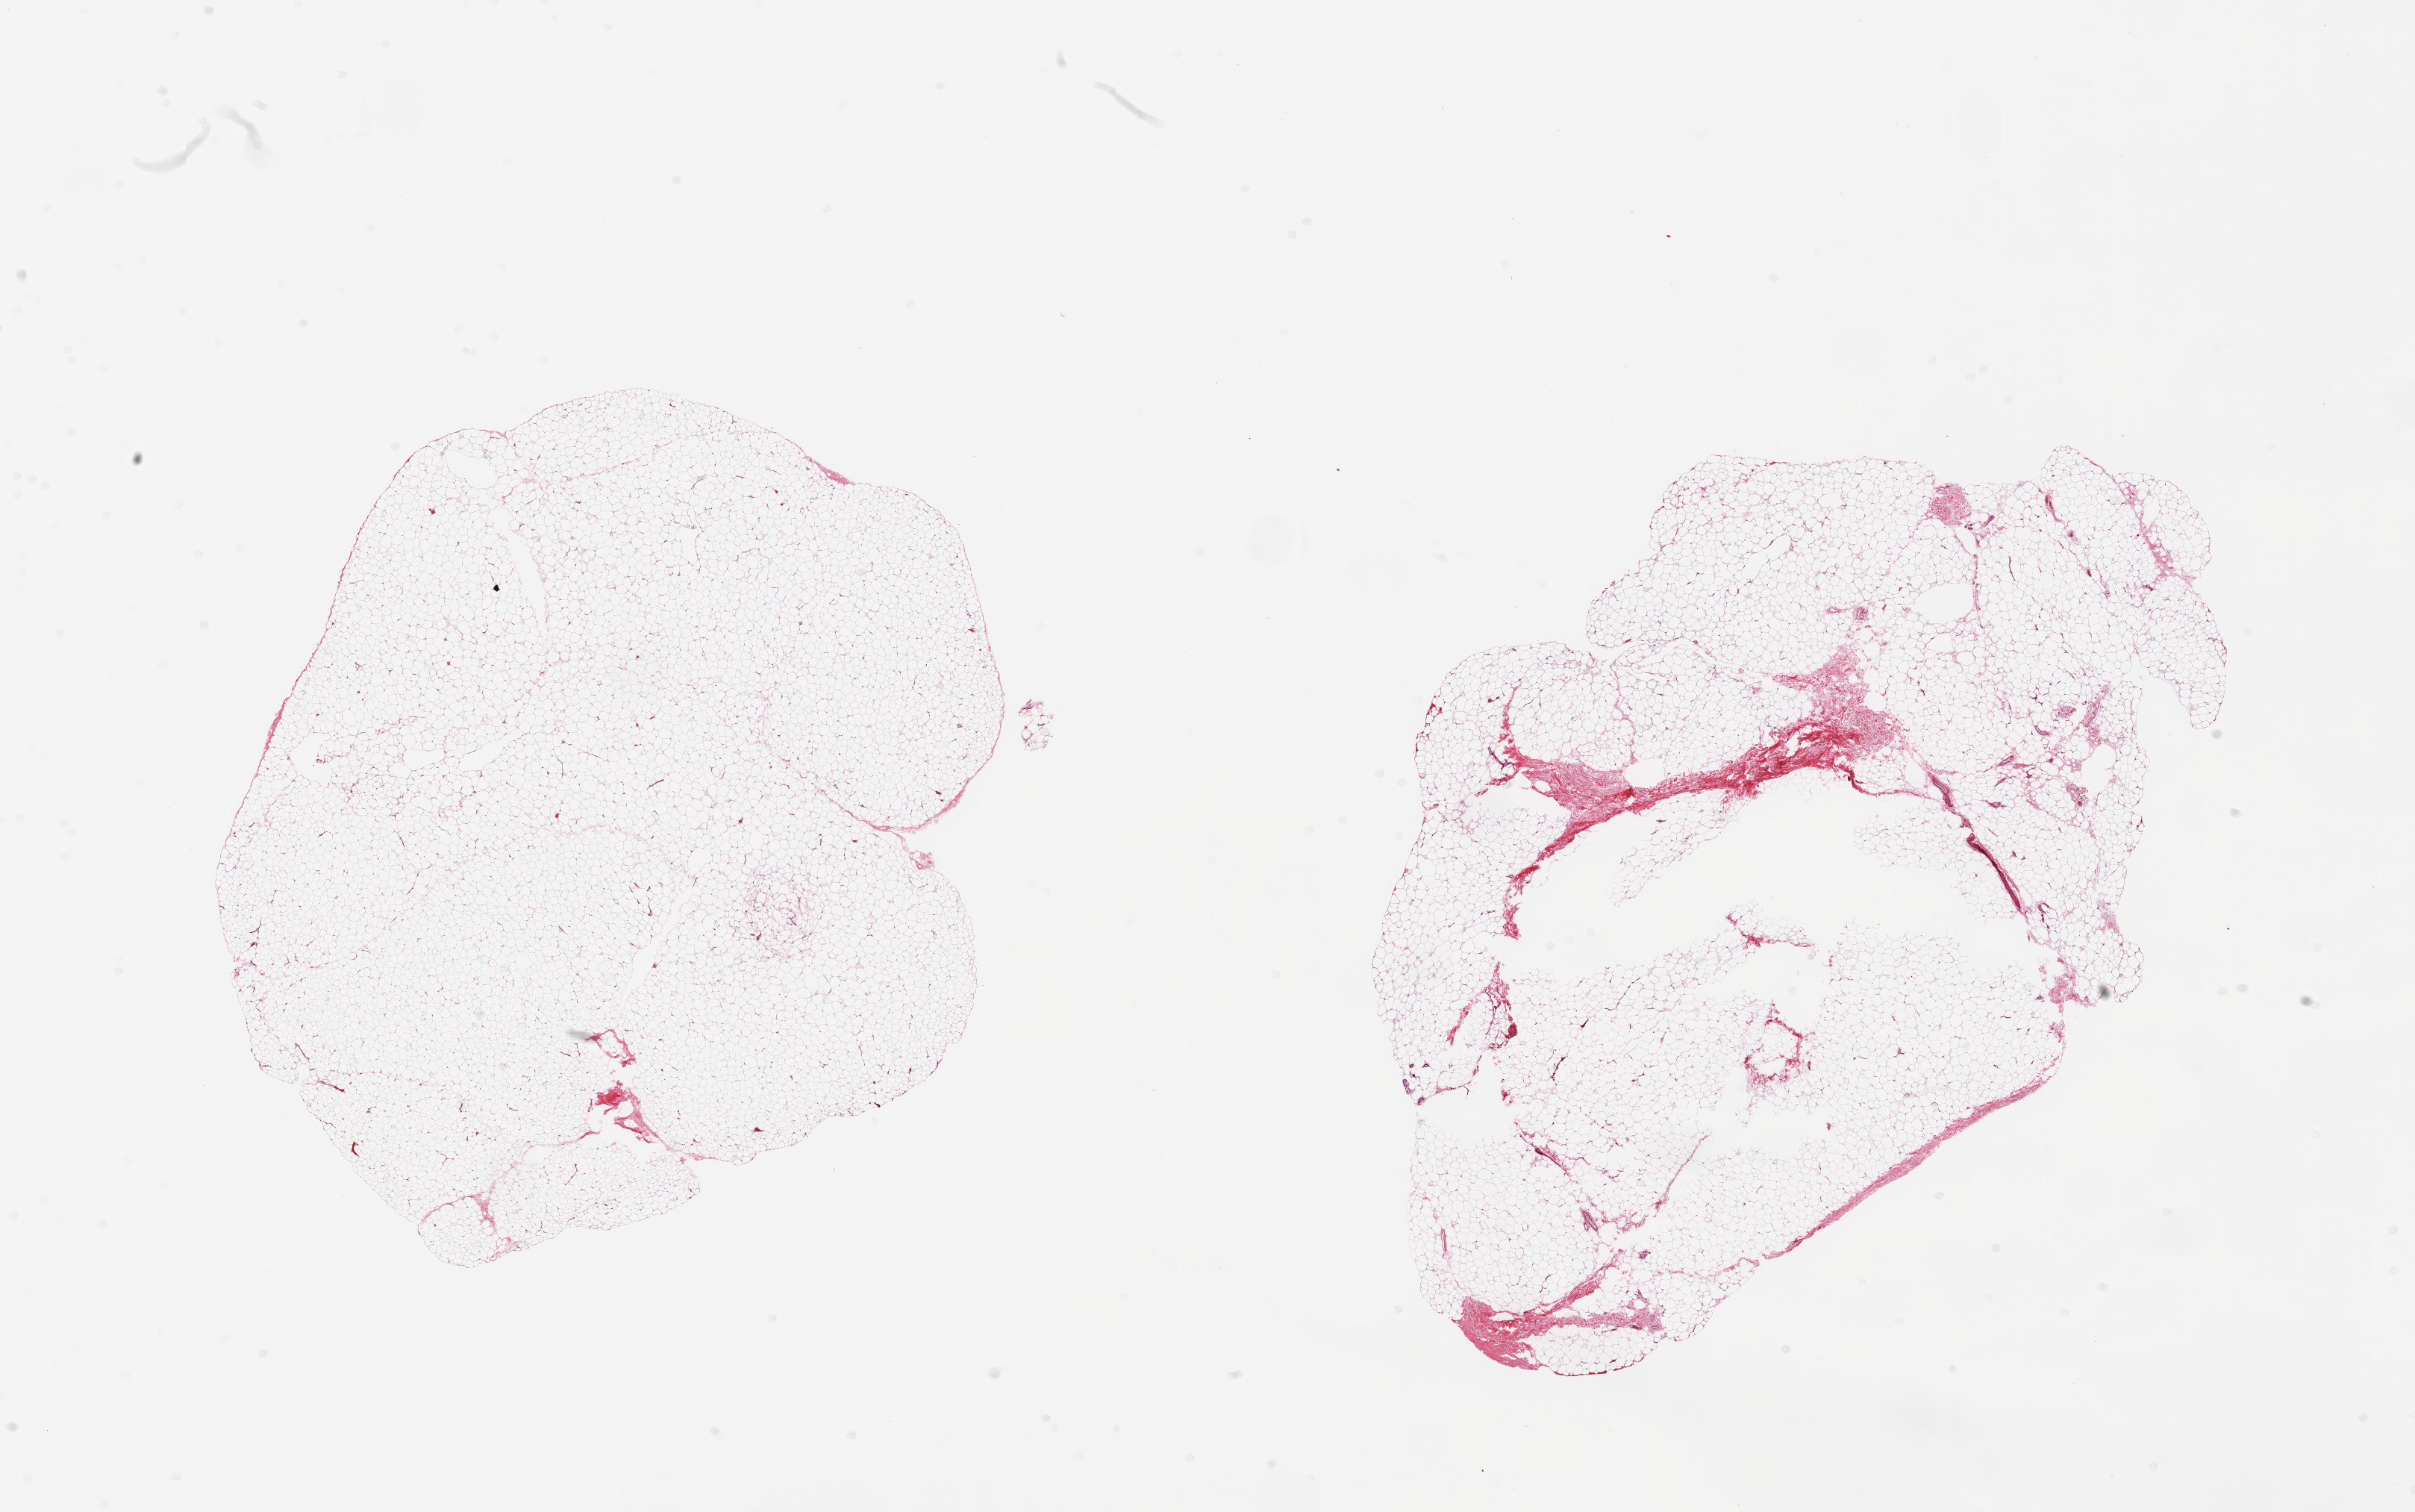
Whole-slide image, hematoxylin and eosin (H&E) stain — whole scanned area (about 25.6 x 16.0 mm) shown as a low-resolution overview; PAXgene-fixed paraffin-embedded (PFPE) section; sampled site (target tissue): adipose tissue; donor tissue sample. Donor sex: male.
Reviewer comment on this tissue sample: 2 pieces; mature adipose tissue, 5--10% fascia, few tissue defects (?poor fixation).